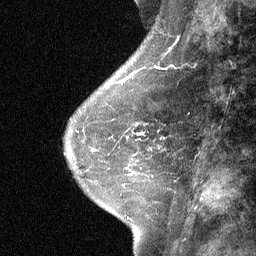
Breast MRI (dynamic contrast-enhanced), one sagittal slice; slice 24 of 64 in the series (ordered by position); dynamic contrast-enhanced study with each time point stored as its own series, time point 2 of 3 at this slice position (early post-contrast, ordered by acquisition time); 1.5 T; TE 4.8 ms, TR 27 ms; 2 mm slice thickness; 256 × 256 image matrix, field of view 180 × 180 mm. Patient: female, 42 years. From the clinical record (not read from this slice): setting: breast cancer imaged before/during neoadjuvant chemotherapy; receptor status: triple-negative.
Structures marked on this image (semi-automatically segmented with operator editing):
- analysis volume of interest (the breast-tissue region the enhancement analysis was run in; not a lesion): box from (x=99, y=117) to (x=167, y=187) px
- tumour enhancement mask (voxels above the 90 % enhancement threshold inside the analysis volume of interest): (x=139, y=133)–(x=143, y=135)